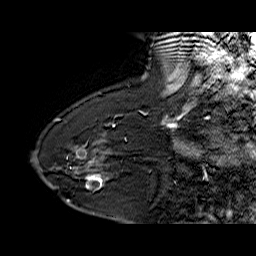
Breast MRI (dynamic contrast-enhanced), one sagittal slice. Slice 45 of 60 in the series (ordered by position). Dynamic contrast-enhanced series, time point 2 of 6 at this slice position (early post-contrast). 1.5 T. TE 6.4 ms, TR 32.9 ms. 4 mm slice thickness. 256 × 256 image matrix, field of view 200 × 200 mm. Female patient. From the clinical record (not read from this slice): setting: breast cancer imaged before/during neoadjuvant chemotherapy; receptor status: HR-positive, HER2-negative.
Structures marked on this image (semi-automatically segmented with operator editing):
- analysis volume of interest (the breast-tissue region the enhancement analysis was run in; not a lesion): box from (x=68, y=154) to (x=125, y=203) px
- tumour enhancement mask (voxels above the 100 % enhancement threshold inside the analysis volume of interest): (x=77, y=156)–(x=108, y=190)